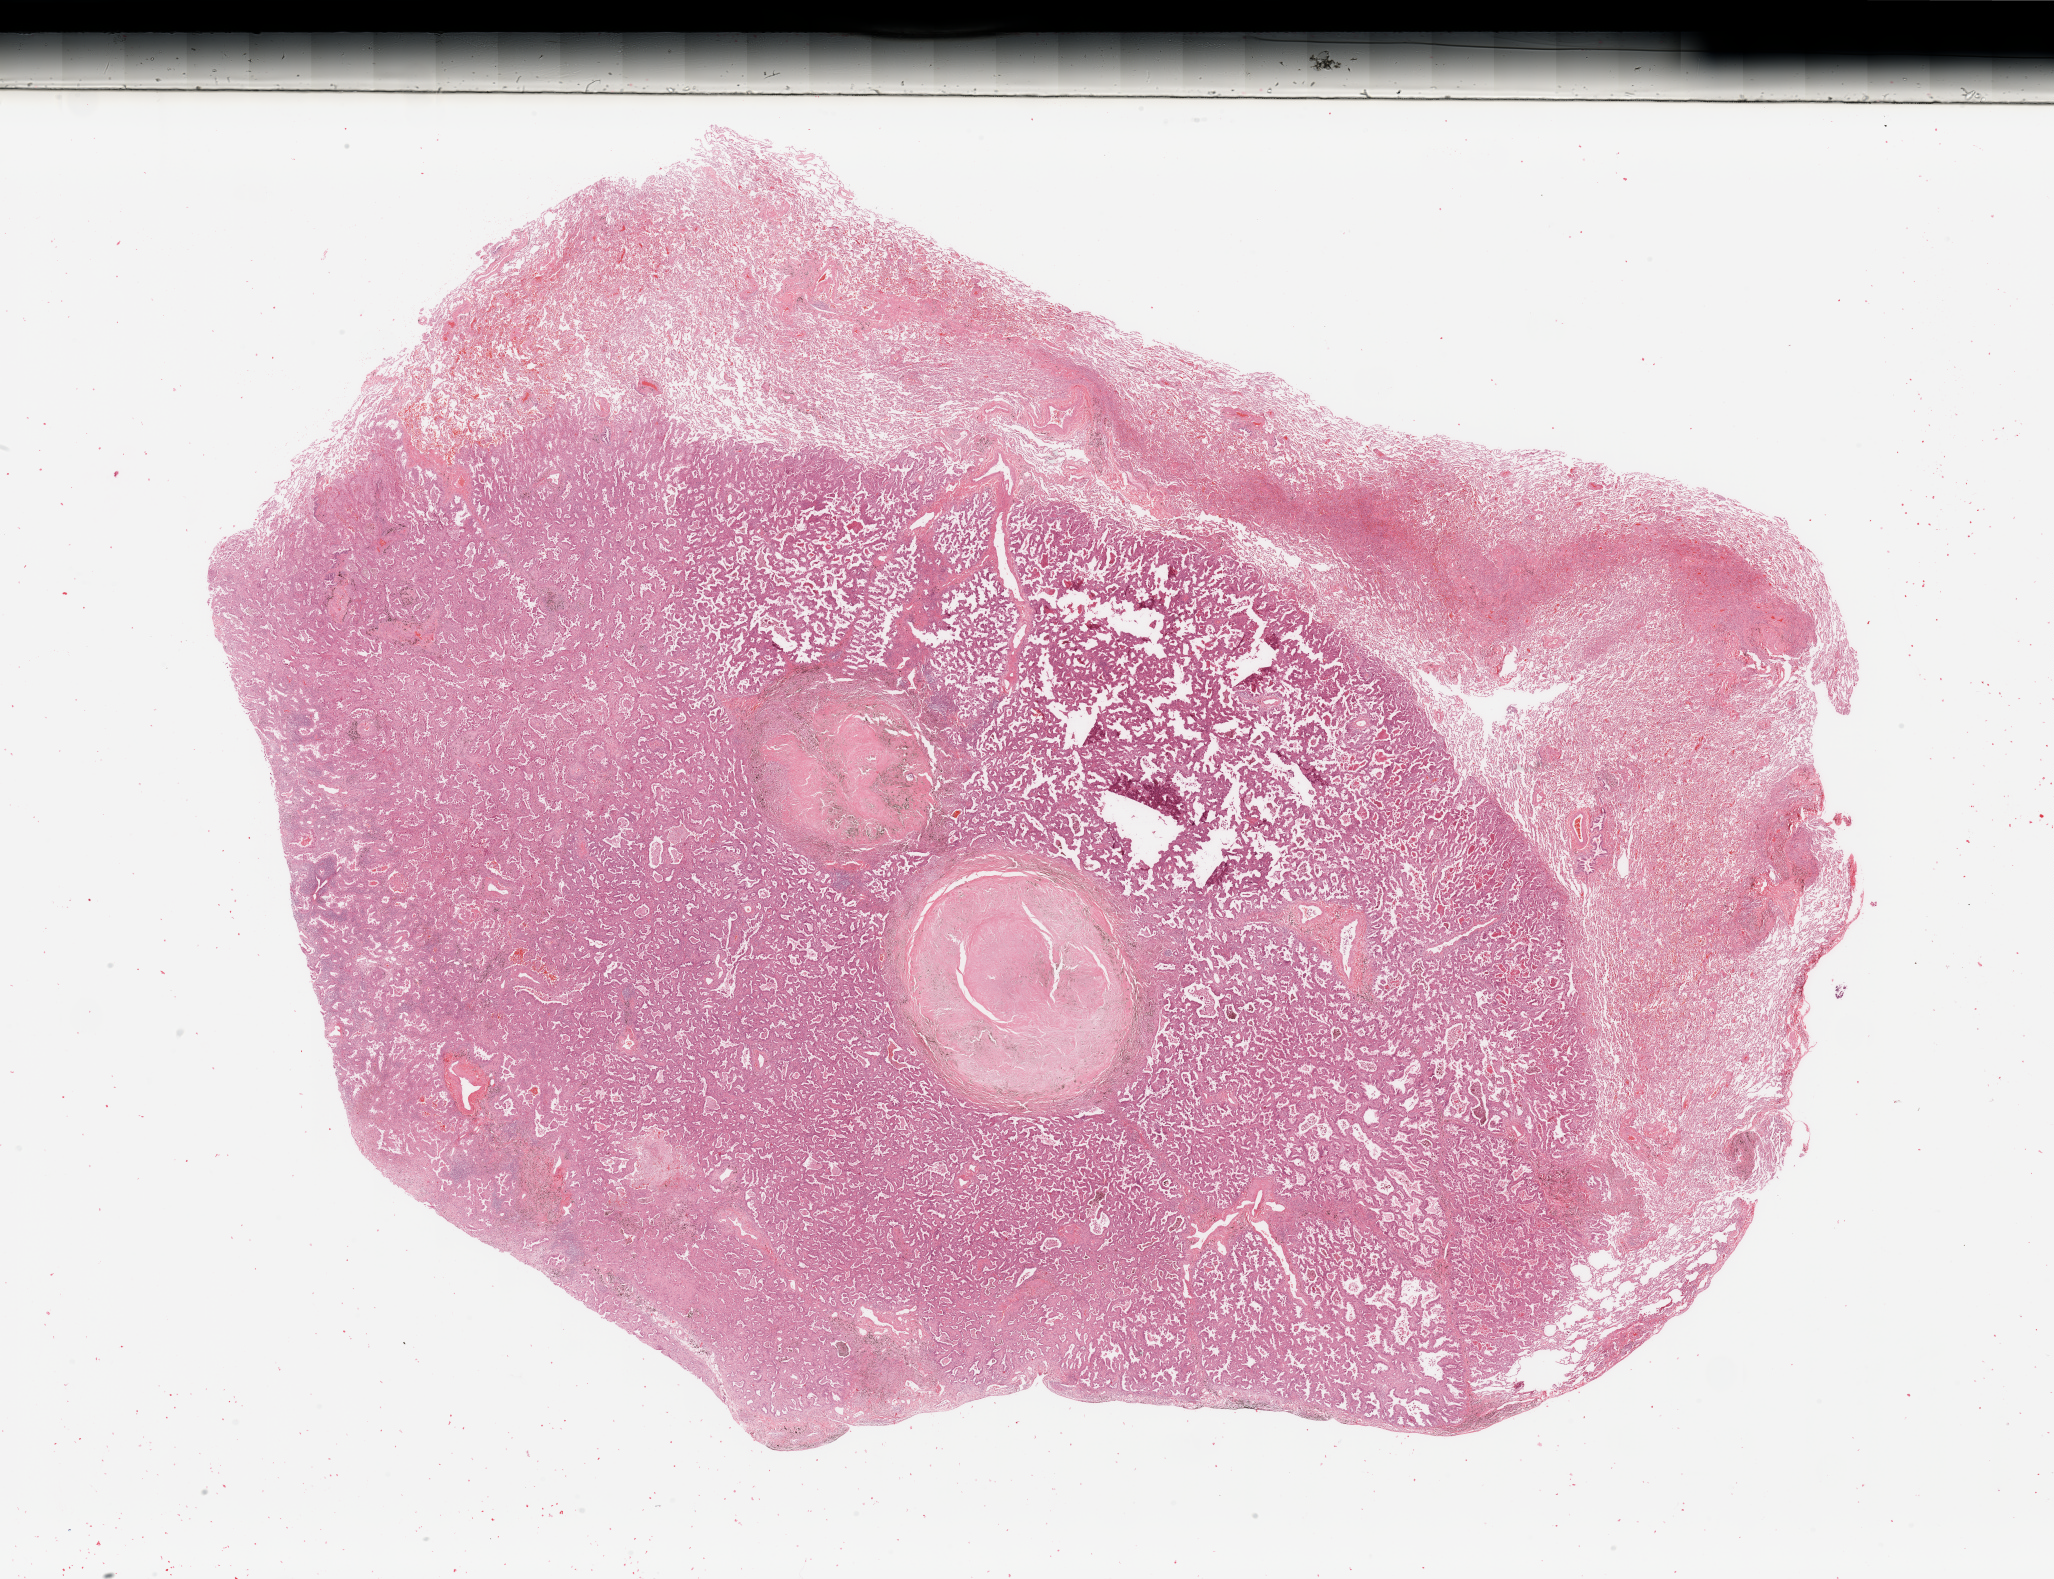
Whole-slide histology image, Hematoxylin and eosin (H&E) stained — whole scanned area (about 32.5 x 25.0 mm, acquisition: 20x scan) shown as a low-resolution overview, tumour tissue sample, sampled site: lung. Patient: male, age 64 years. Histologic grade: G2 (moderately differentiated). Pathologist review of this section (percent, as recorded): tumour nuclei 70%, necrosis 20%.
Diagnosis: Adenocarcinoma, NOS. AJCC pathologic stage: IIA. Primary tumour site (as recorded): right lower lobe.